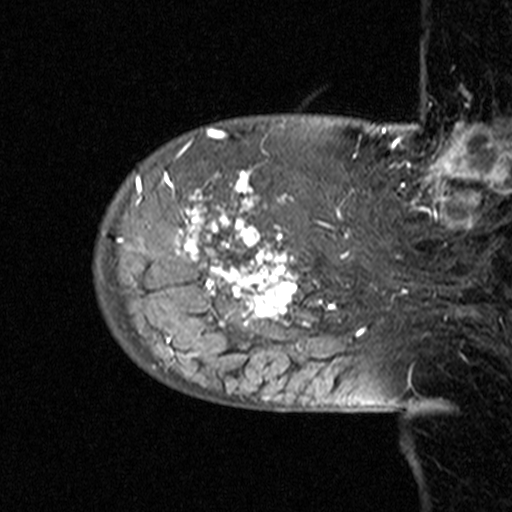
Breast MRI (dynamic contrast-enhanced), one sagittal slice. Slice 9 of 44 in the series (ordered by position). Dynamic contrast-enhanced study with each time point stored as its own series, time point 2 of 3 at this slice position (early post-contrast, ordered by acquisition time). 1.5 T. TE 4.5 ms, TR 11 ms. 512 × 512 image matrix, field of view 200 × 200 mm. Patient: female, 53 years. Case-level facts recorded for this patient, not image findings: setting: breast cancer imaged before/during neoadjuvant chemotherapy; receptor status: HR-positive, HER2-negative.
Outlined on this slice (semi-automatic segmentation, software-assisted and operator-edited):
- analysis volume of interest (the breast-tissue region the enhancement analysis was run in; not a lesion): bounding box <93,140,311,353> (left, top, right, bottom; pixels)
- tumour enhancement mask (voxels above the 90 % enhancement threshold inside the analysis volume of interest): <118,171,305,324>